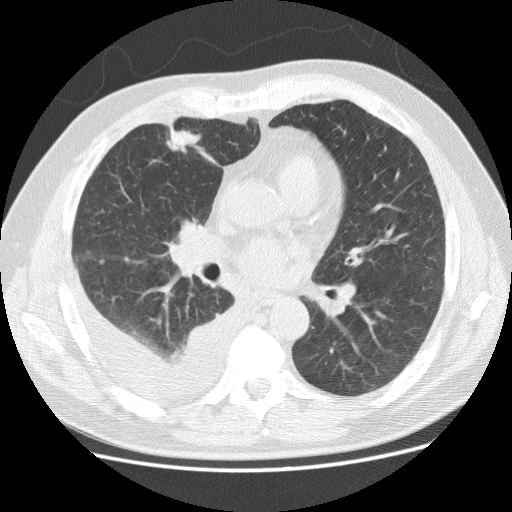
Low-dose screening chest CT, axial slice; first (baseline) screen; lung window (W 1500 / L -600 HU); slice 77 of 142 in the series. Male participant, aged 65 years at enrolment. Current smoker at enrolment.
• Expert reader's lesion annotation, bounding box (x1, y1, x2, y2) in pixels: (149, 120, 216, 170).
• Reader record for this screening exam (exam-level; its link to the box is not recorded): non-calcified nodule or mass ≥4 mm, right middle lobe, 22 × 15 mm, spiculated (stellate) margins, mixed attenuation.
• Later outcome: lung cancer diagnosed 4 days after this screen — adenocarcinoma, NOS, right middle lobe, stage IV (AJCC 6th edition), 20 mm at pathology.